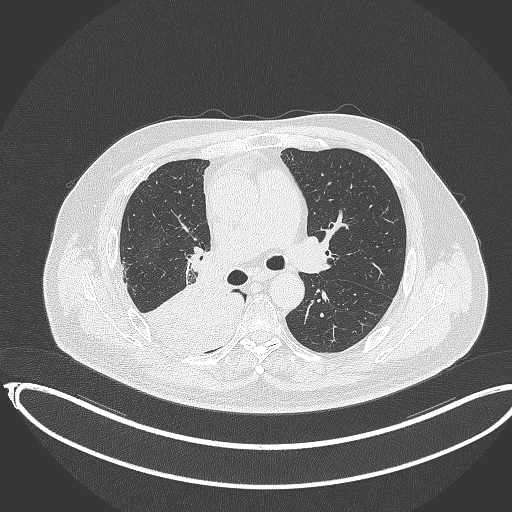
Chest CT, one axial slice; position 213 of 403 along the scan axis; 120 kVp; lung window (W 1500 / L -600 HU); 1 mm slice thickness; 512 × 512 image matrix. Male patient, age 68 years. Case-level facts recorded for this patient, not image findings: clinical TNM (as recorded): T2a N0 M0.
Outlined on this slice (bounding box drawn by a radiologist):
- lung tumour (recorded histology: adenocarcinoma): bounding box [x1, y1, x2, y2] px = [142, 281, 244, 355]